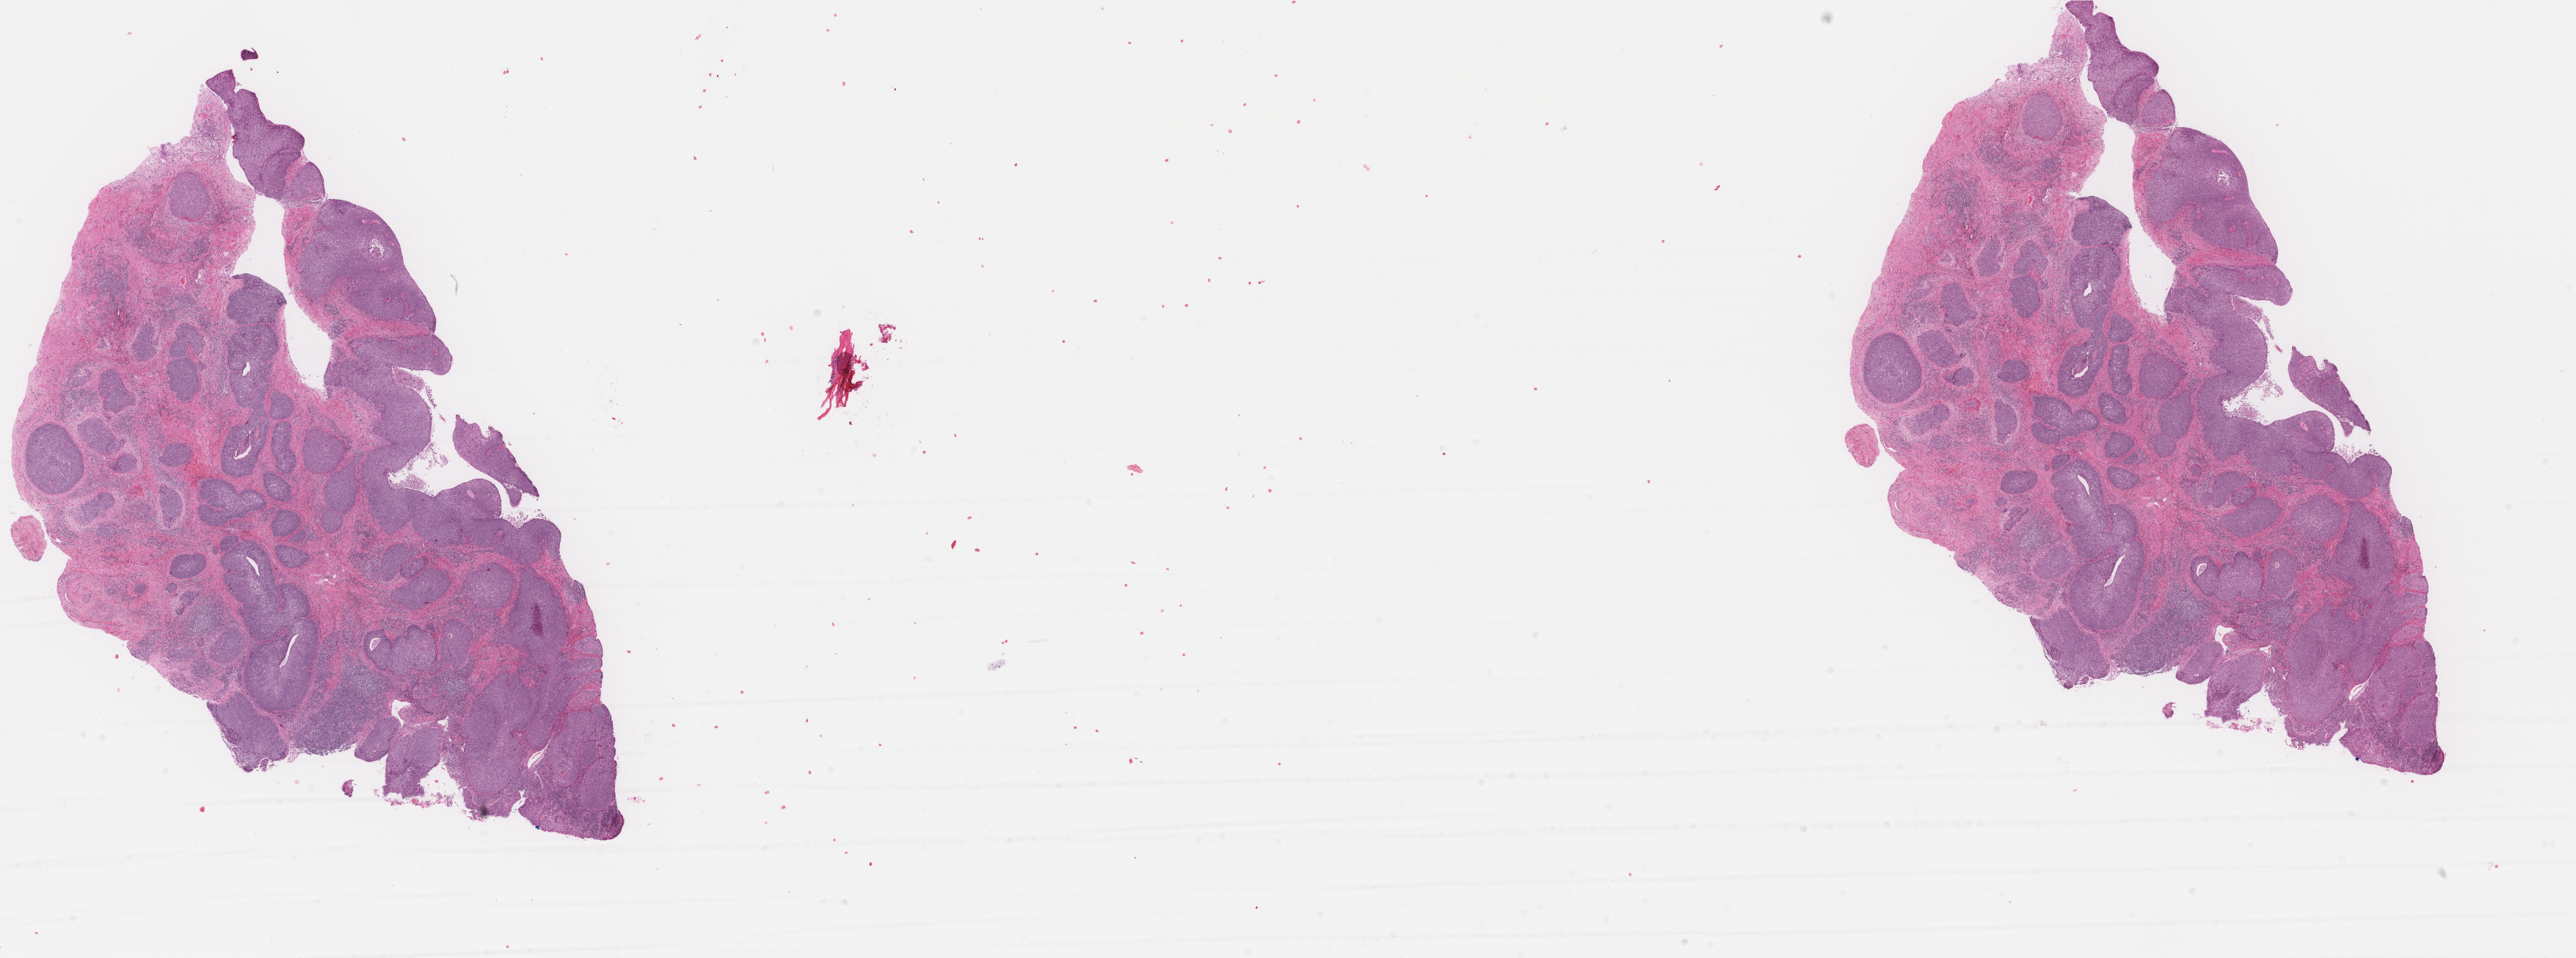
Whole-slide histology image, H&E-stained — whole scanned area (about 27.9 x 10.4 mm) shown as a low-resolution overview, formalin-fixed paraffin-embedded (FFPE) diagnostic section, primary tumour sample from the cervix. Patient: female, age at initial diagnosis 58 years. Histologic grade: G3 (poorly differentiated).
FIGO stage: IIB. Diagnosis: Squamous cell carcinoma, NOS (cervix uteri).